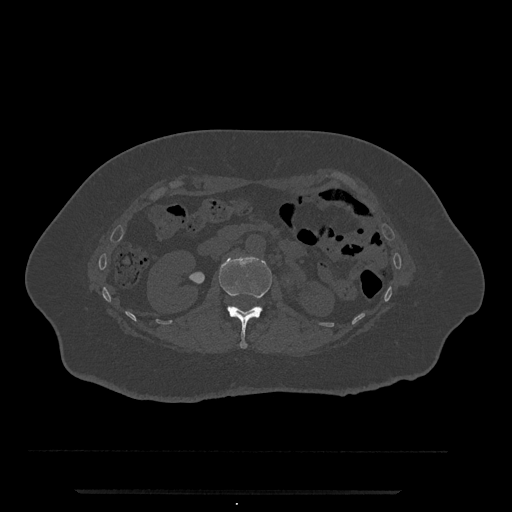
CT including the spine, one axial slice; position 94 of 797 along the scan axis; reconstruction kernel Br40s/3; 120 kVp; bone window (W 1800 / L 400 HU); 512 × 512 image matrix, field of view 440 × 440 mm. Patient: female, 51 years. From the clinical record (not read from this slice): primary cancer: neuro; vertebrae with lytic lesions (as recorded): T8.
Outlined on this slice (semi-automatically segmented with operator editing):
- L1 vertebra: bounding box (x1, y1, x2, y2) in pixels: (219, 255, 272, 349)